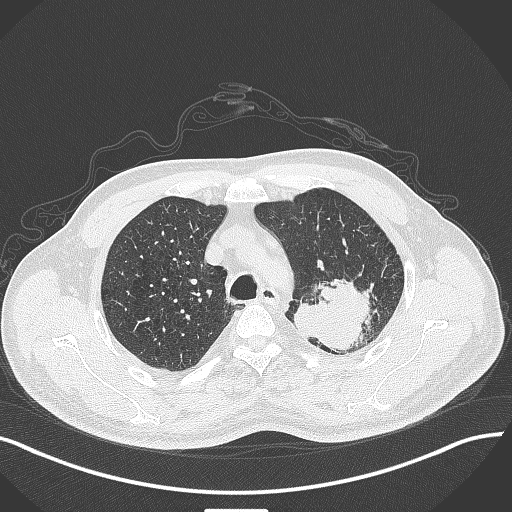
Chest CT, one axial slice. Reconstruction kernel B70f. 120 kVp. Lung window (W 1500 / L -600 HU). 512 × 512 image matrix, field of view 400 × 400 mm. Male patient, age 55 years. From the clinical record (not read from this slice): clinical TNM (as recorded): T3 N0 M1c.
Structures marked on this image (rectangle marked by the reading radiologist):
- lung tumour (recorded histology: adenocarcinoma): bounding box <292,270,387,361> (left, top, right, bottom; pixels)